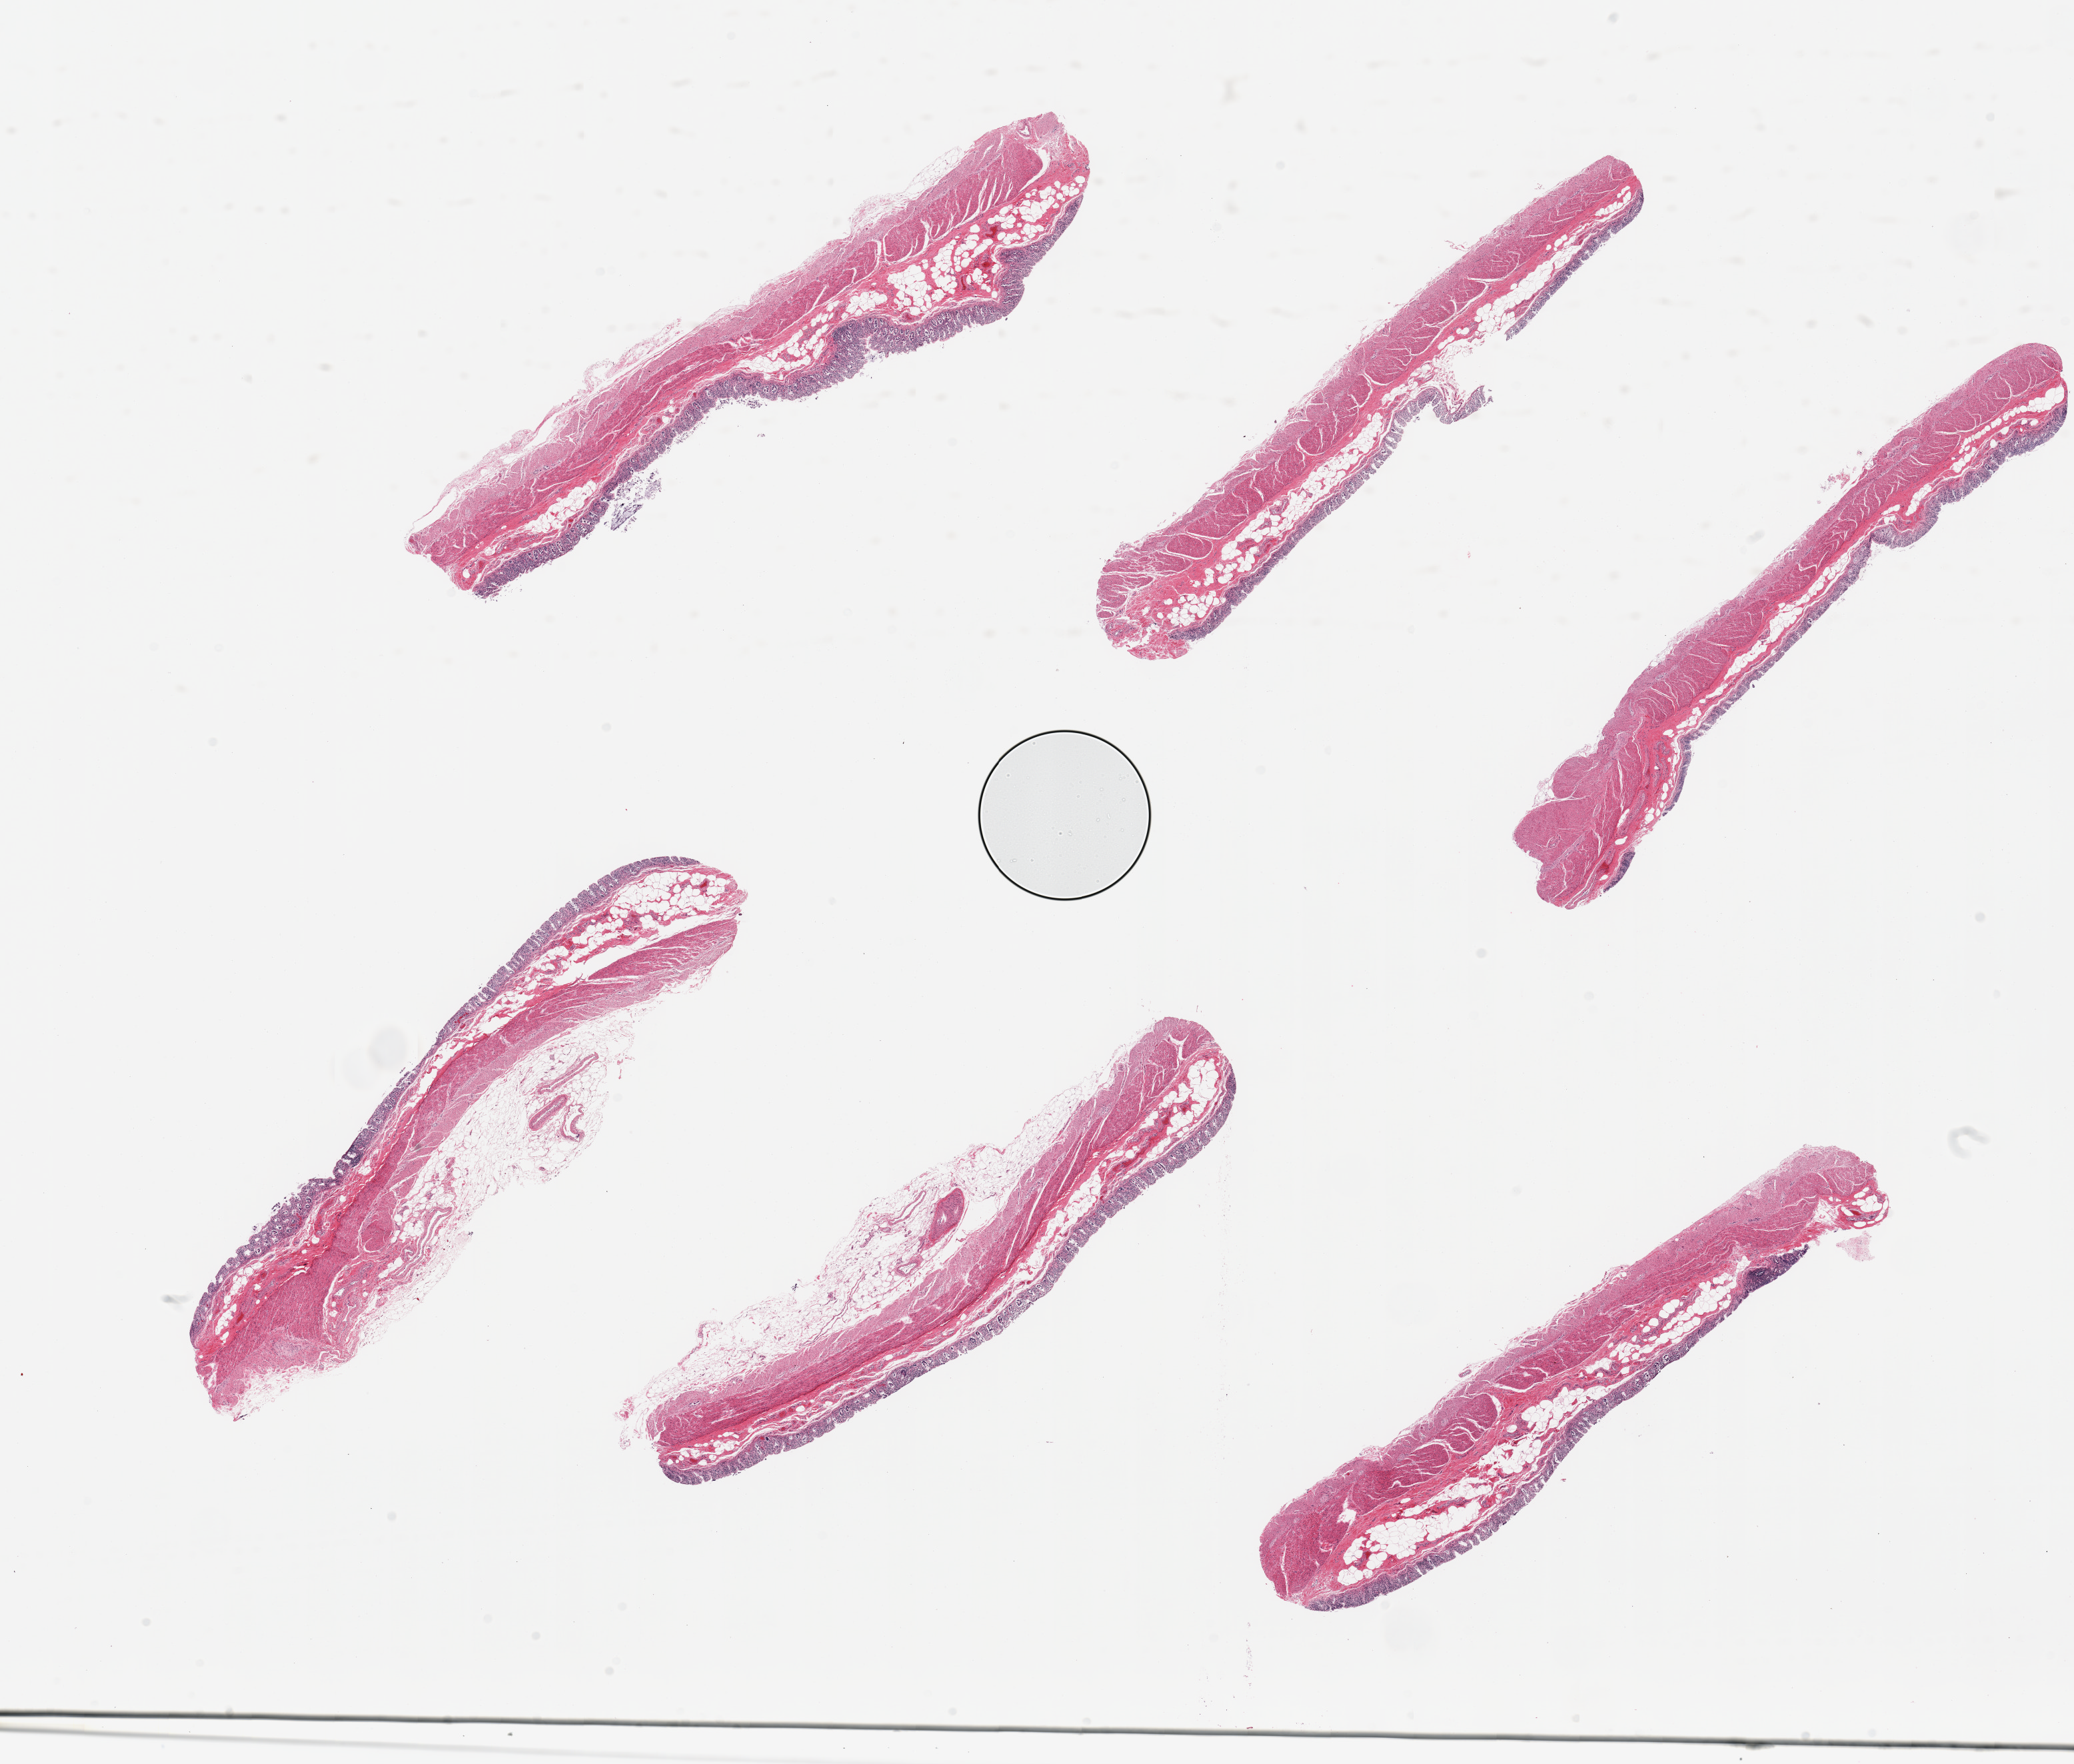
Digitized hematoxylin and eosin (H&E)-stained section — a low-resolution overview of the entire scanned area, about 24.6 x 20.9 mm (slide scanned at 20x), PAXgene-fixed, paraffin-embedded tissue, sampled site (target tissue): transverse colon, donor tissue sample. Male donor.
Pathologist's review note for this sample: 6 pieces; glands autolyzed; muscle preserved; 2 have excessive perimuscular fat.